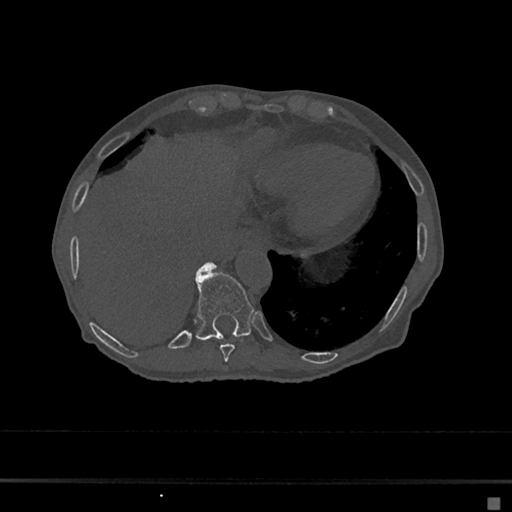
CT including the spine, one axial slice. Slice 240 of 797 in the series (ordered by position). Reconstruction kernel Br40s/3. 120 kVp. Bone window (W 1800 / L 400 HU). 0.5 mm slice thickness. 512 × 512 image matrix, field of view 360 × 360 mm. Patient: female, 68 years. Case-level facts recorded for this patient, not image findings: primary cancer: renal.
Annotated regions visible in this slice (semi-automatically segmented with operator editing):
- T10 vertebra: box from (x=196, y=264) to (x=254, y=341) px
- T11 vertebra: (x=198, y=266)–(x=204, y=272)
- T9 vertebra: (x=220, y=340)–(x=242, y=362)